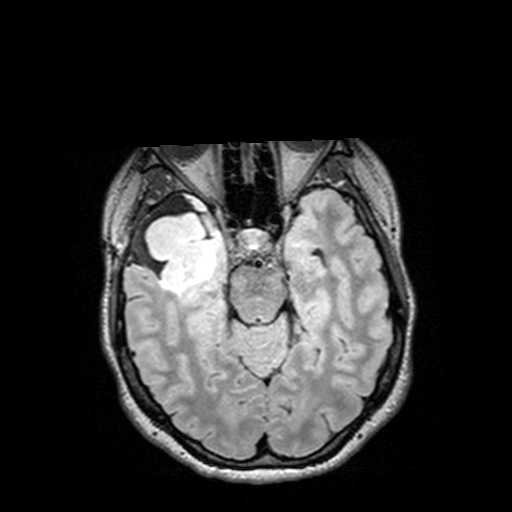
Brain MRI from a brain-tumour surgery series, one axial slice. Slice 92 of 144 in the series (ordered by position). T2 FLAIR. 512 × 512 image matrix, field of view 250 × 250 mm. Case-level facts recorded for this patient, not image findings: histopathology: Astrocytoma; WHO grade: 3; IDH mutation: yes.
Outlined on this slice (manually delineated by an expert):
- tumour: bounding box [x1, y1, x2, y2] px = [126, 193, 232, 292]